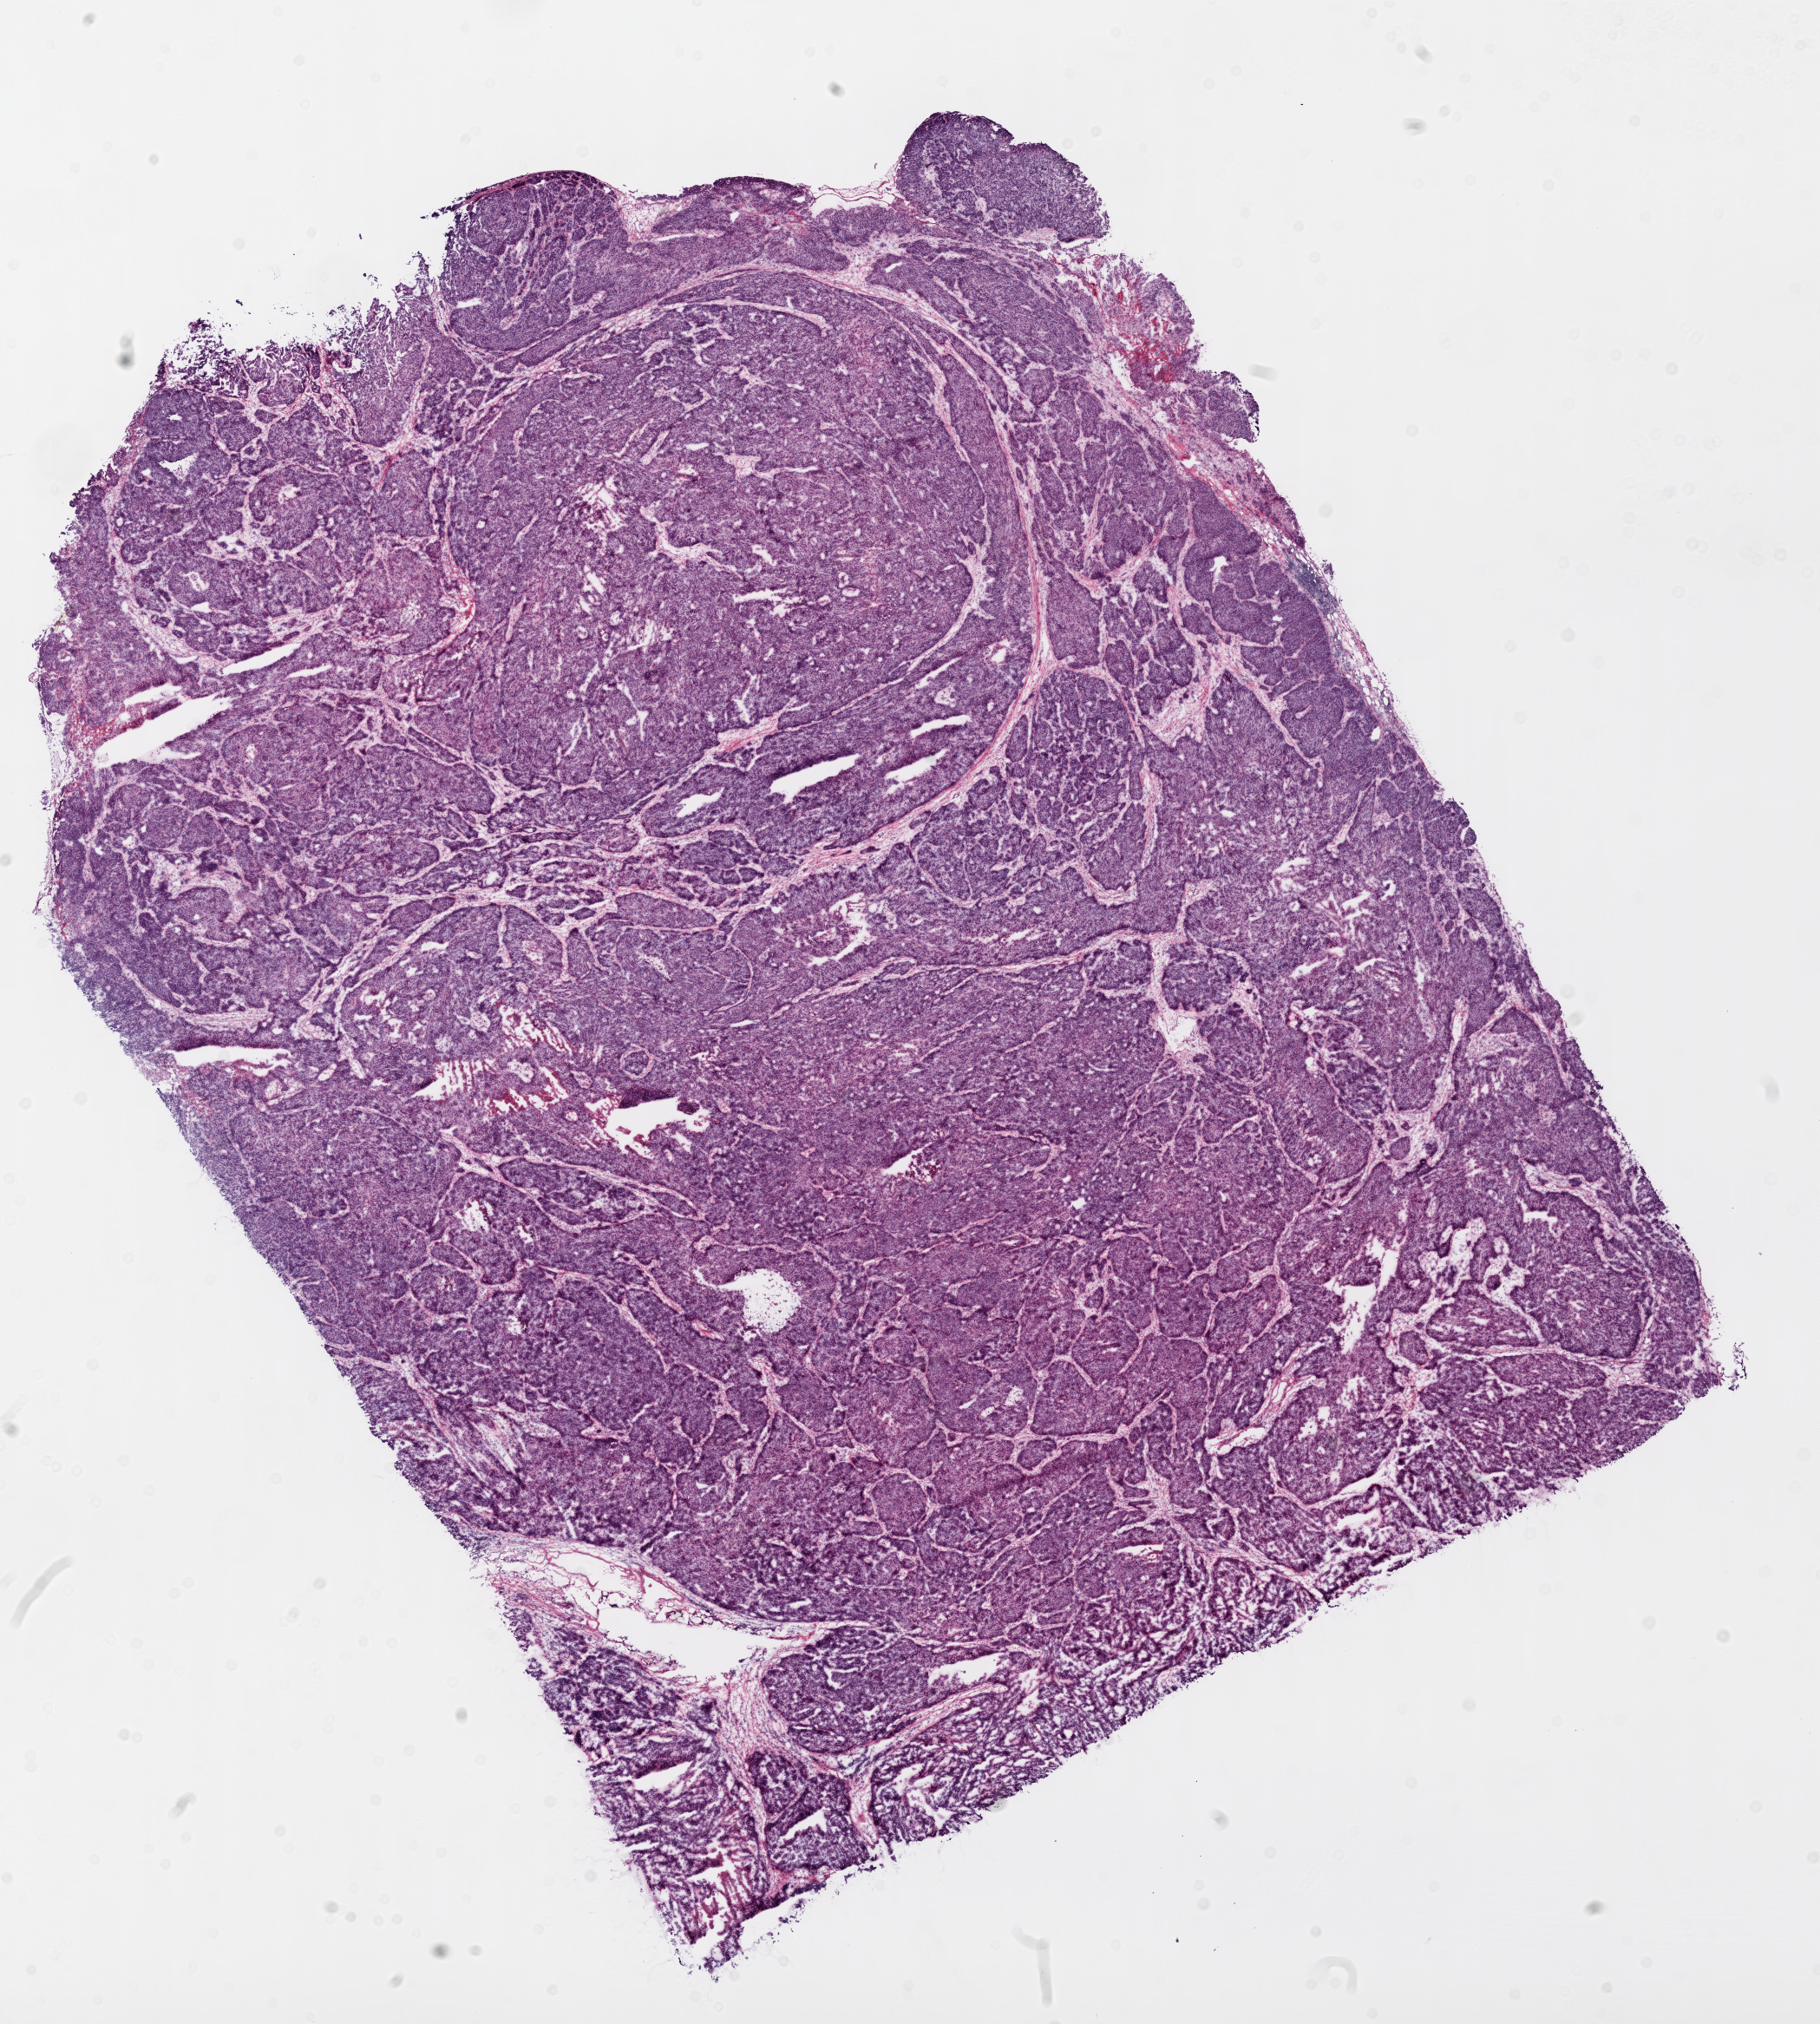
H&E whole-slide image, shown as a low-resolution overview of the whole scanned area (about 16.9 x 18.8 mm, from a 20x scan). Frozen section. Sample: primary tumour, ovary. Patient: female, age at initial diagnosis 49 years. Histologic grade: G3 (poorly differentiated). Composition of this section per pathologist review: tumour cells 95%, tumour nuclei 98%, normal cells 0%, stromal cells 5%, necrosis 0%.
FIGO stage: IIIC. Pathologic diagnosis: Serous cystadenocarcinoma, NOS.